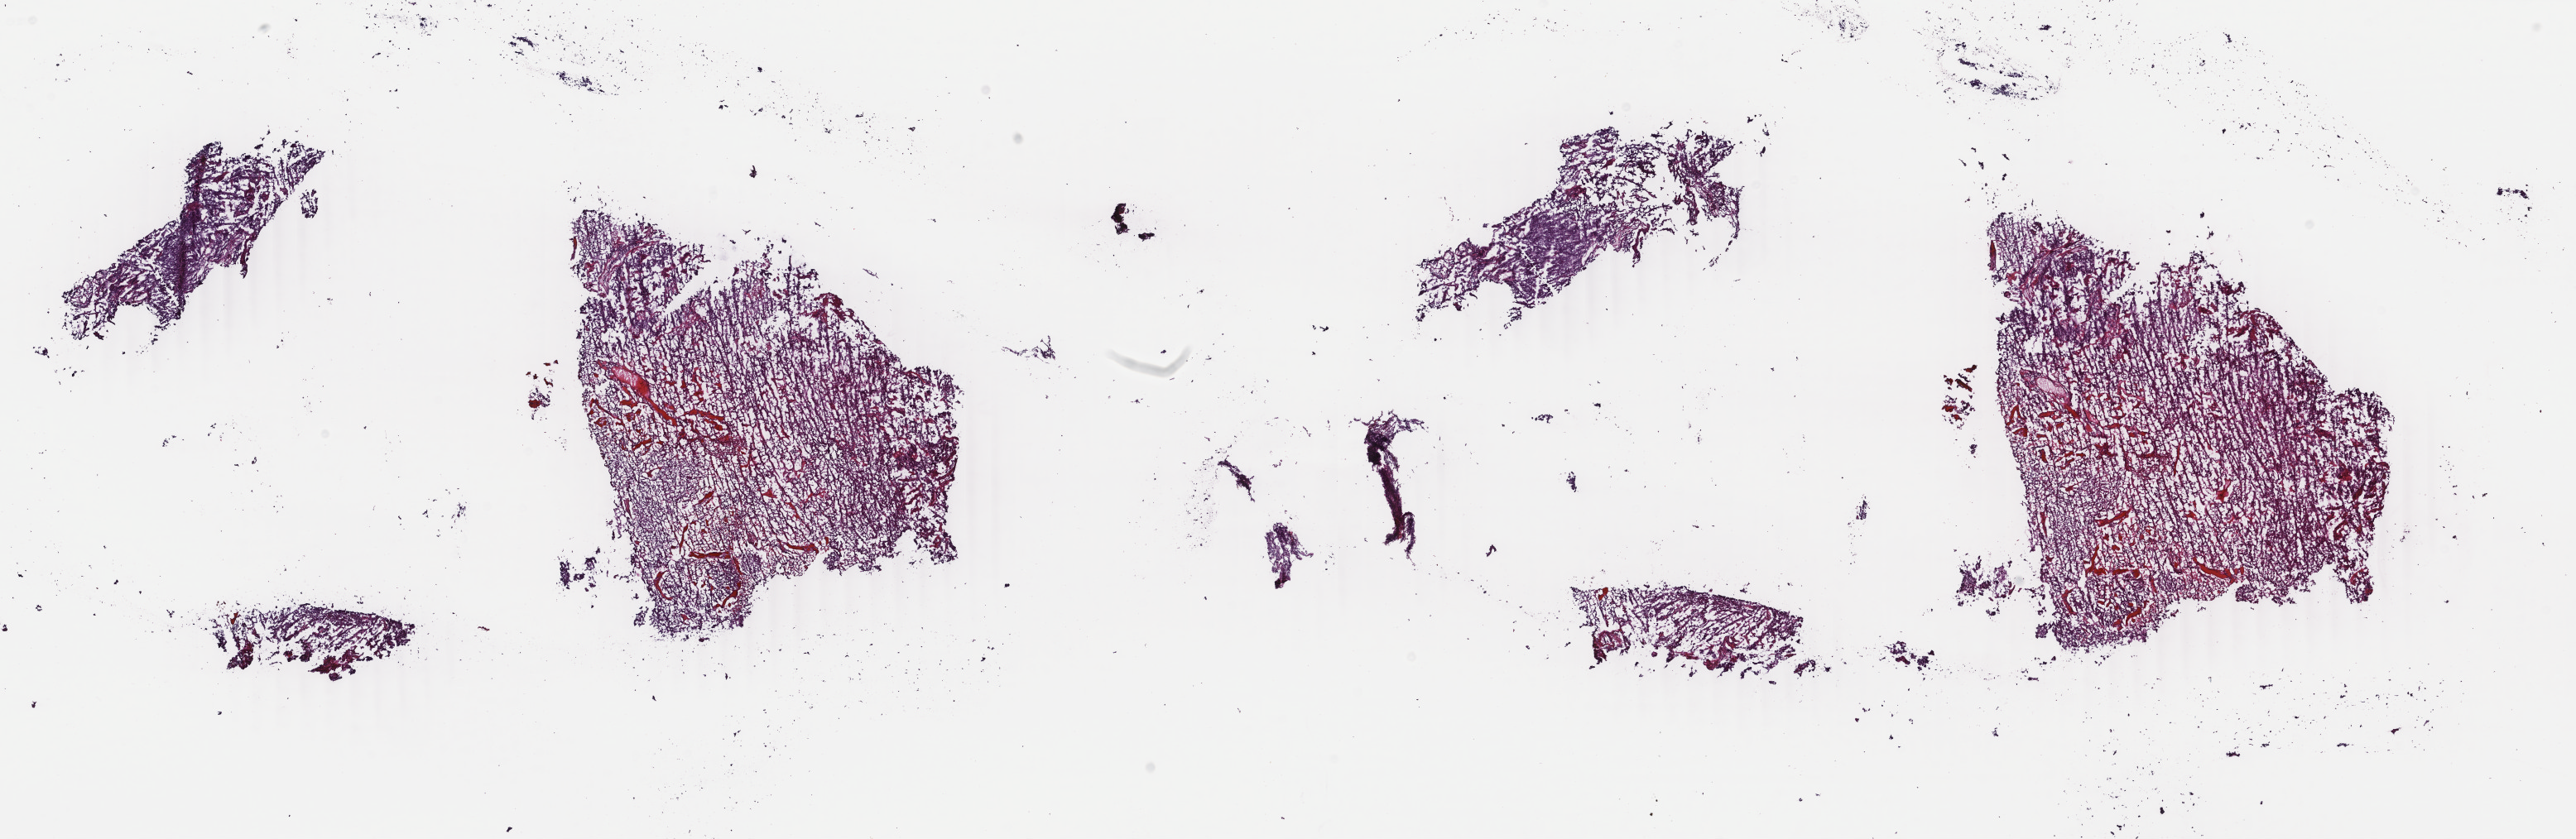
Hematoxylin and eosin (H&E) stained whole-slide image, whole scanned area (about 24.7 x 8.1 mm, acquisition: 40x scan) shown as a low-resolution overview, frozen section, primary tumour sample from the uterus. Patient: female, age at initial diagnosis 51 years. Histologic grade: G3 (poorly differentiated). Pathologist review of this section (percent, as recorded): tumour cells 93%, tumour nuclei 95%, normal cells 0%, stromal cells 5%, necrosis 2%. Inflammatory infiltration, as recorded: lymphocyte infiltration 5%, monocyte infiltration 3%, neutrophil infiltration 0%.
Histologic diagnosis: Endometrioid adenocarcinoma, NOS (endometrium). Lymph nodes positive (case pathology): 0 of 6 examined. FIGO stage: II.